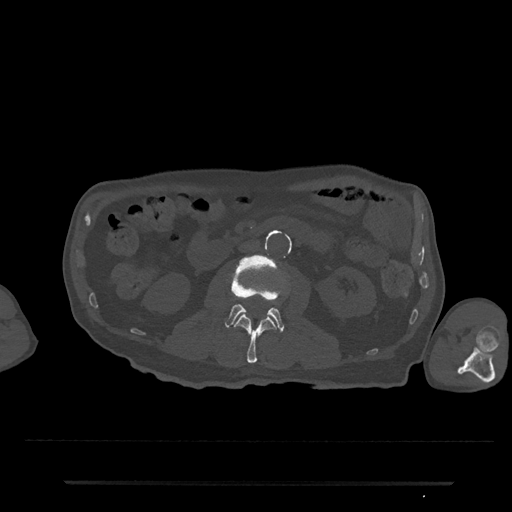
CT including the spine, one axial slice; slice 24 of 797 in the series (ordered by position); 120 kVp; bone window (W 1800 / L 400 HU); 512 × 512 image matrix. Patient: male, 74 years. Case-level facts recorded for this patient, not image findings: primary cancer: prostate.
Outlined on this slice (semi-automatically segmented with operator editing):
- L2 vertebra: box from (x=235, y=315) to (x=276, y=364) px
- L3 vertebra: (x=225, y=255)–(x=285, y=333)